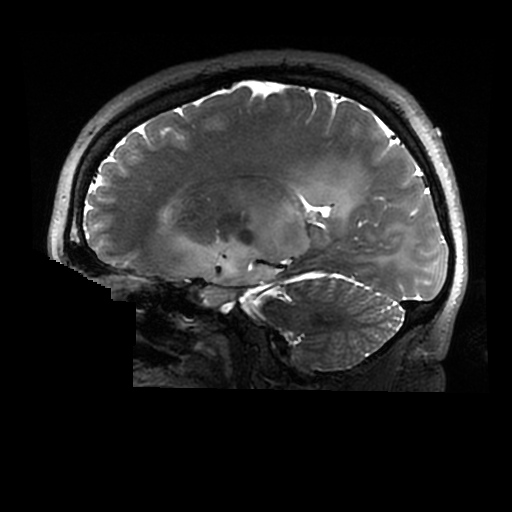
Brain MRI from a brain-tumour surgery series, one sagittal slice; 512 × 512 image matrix, field of view 240 × 240 mm. From the clinical record (not read from this slice): histopathology: Astrocytoma; WHO grade: 2; IDH mutation: yes.
Structures marked on this image (manually delineated by an expert):
- tumour: bounding box (x1, y1, x2, y2) in pixels: (179, 191, 354, 307)